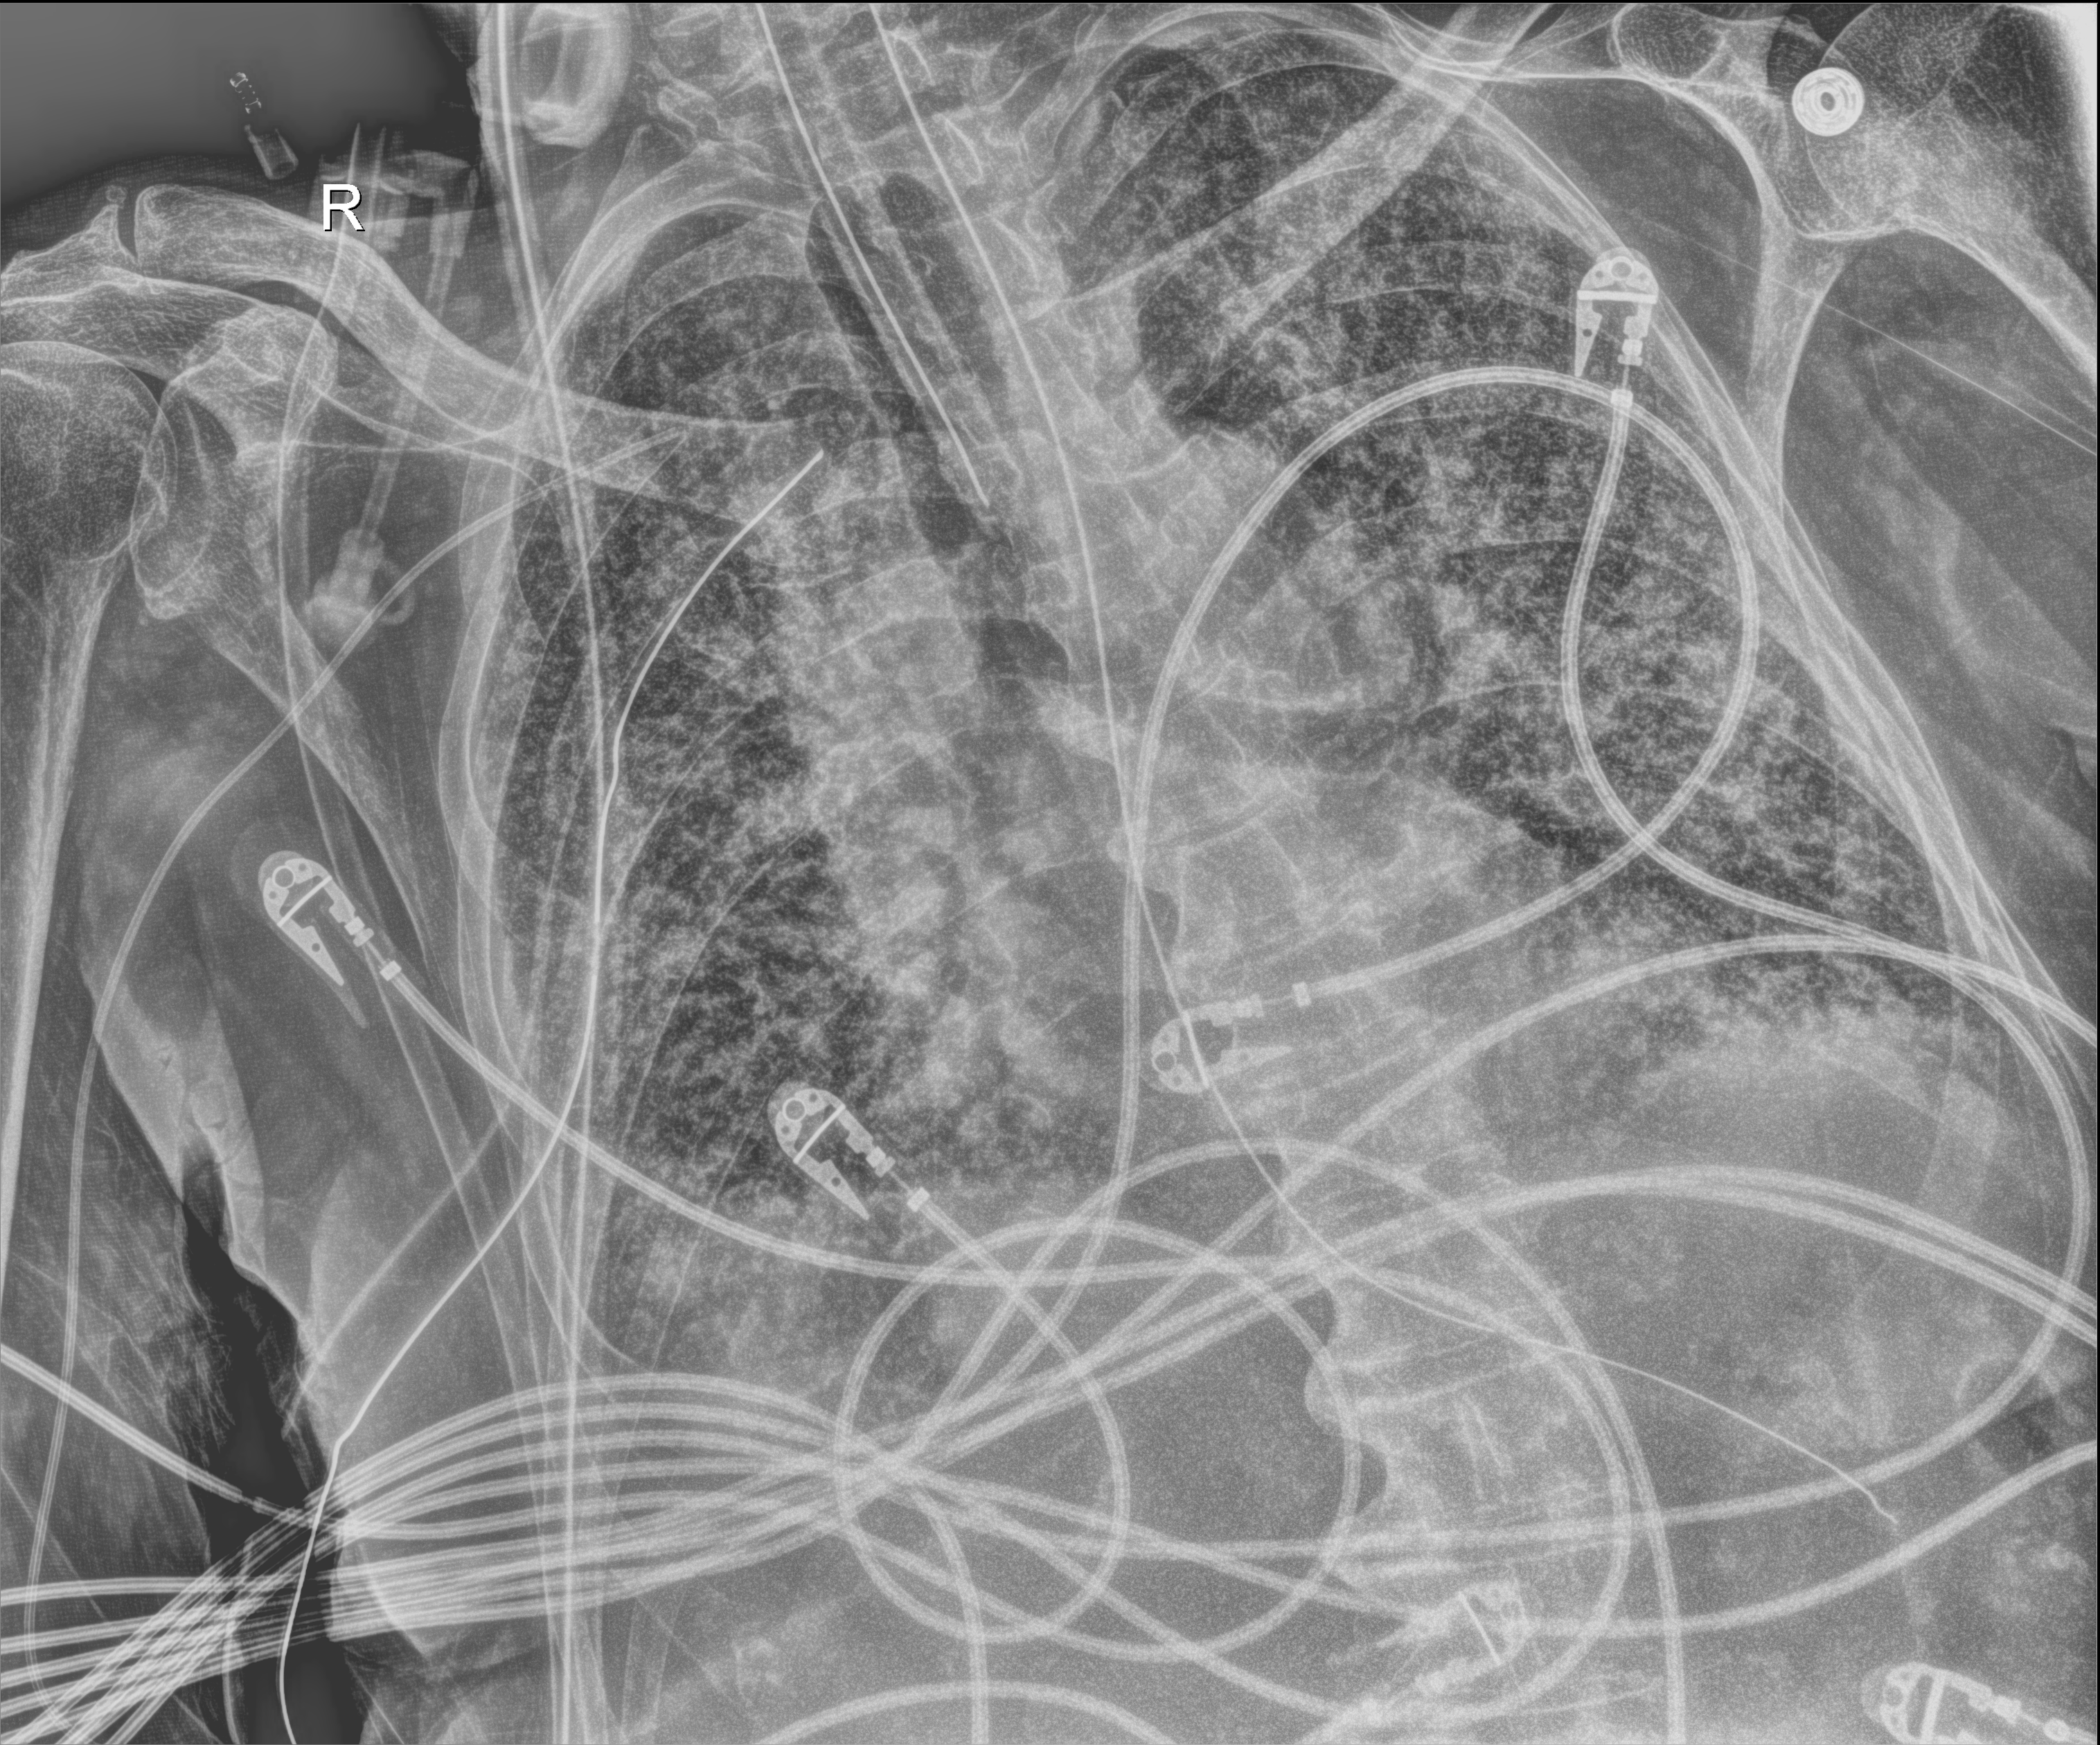
Bedside chest radiograph (digital radiography); anteroposterior (AP) projection. Male patient hospitalised with COVID-19, age 75–90 years.
Admission-level facts for this patient (not findings on this image; timing relative to this image not recorded): smoking status (admission record): never.